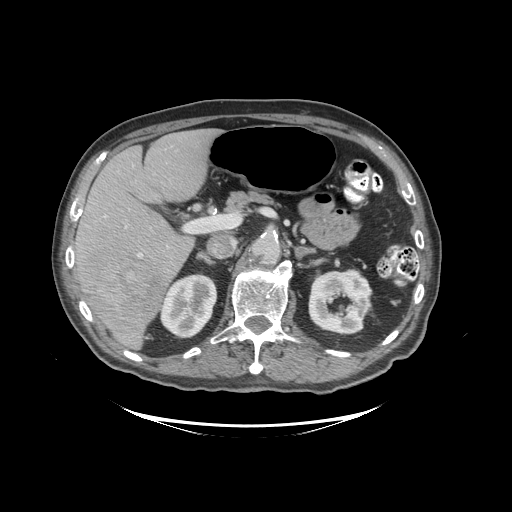
Contrast-enhanced abdominal CT (liver protocol), one axial slice; slice 56 of 99 in the series (ordered by position); soft-tissue window (W 400 / L 40 HU); 2.5 mm slice thickness; 512 × 512 image matrix, field of view 460 × 460 mm. From the clinical record (not read from this slice): diagnosis: hepatocellular carcinoma (patient treated with transarterial chemoembolisation; whether this scan precedes or follows treatment is not stated here); TNM stage (as recorded): Stage-I; Child-Pugh class: A; tumour nodularity: uninodular.
Annotated regions visible in this slice (semi-automatic segmentation, software-assisted and operator-edited):
- liver parenchyma outside the tumour (the mass and vessels are separate outlines, so this box may not span the whole liver): bounding box [x1, y1, x2, y2] px = [70, 128, 216, 348]
- mass: [83, 254, 163, 337]
- liver vessels: [71, 215, 142, 260]